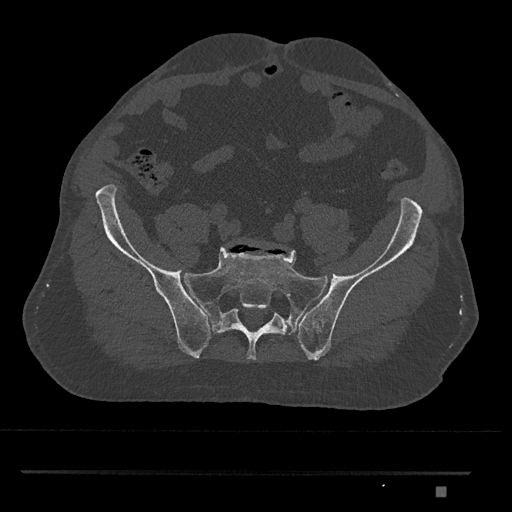
CT including the spine, one axial slice. Slice 491 of 1134 in the series (ordered by position). Reconstruction kernel Br40s/3. 120 kVp. Bone window (W 1800 / L 400 HU). 0.5 mm slice thickness. 512 × 512 image matrix, field of view 429 × 429 mm. Male patient, age 65 years. Case-level facts recorded for this patient, not image findings: primary cancer: prostate.
Annotated regions visible in this slice (semi-automatically segmented with operator editing):
- L5 vertebra: bounding box [x1, y1, x2, y2] px = [254, 243, 276, 248]